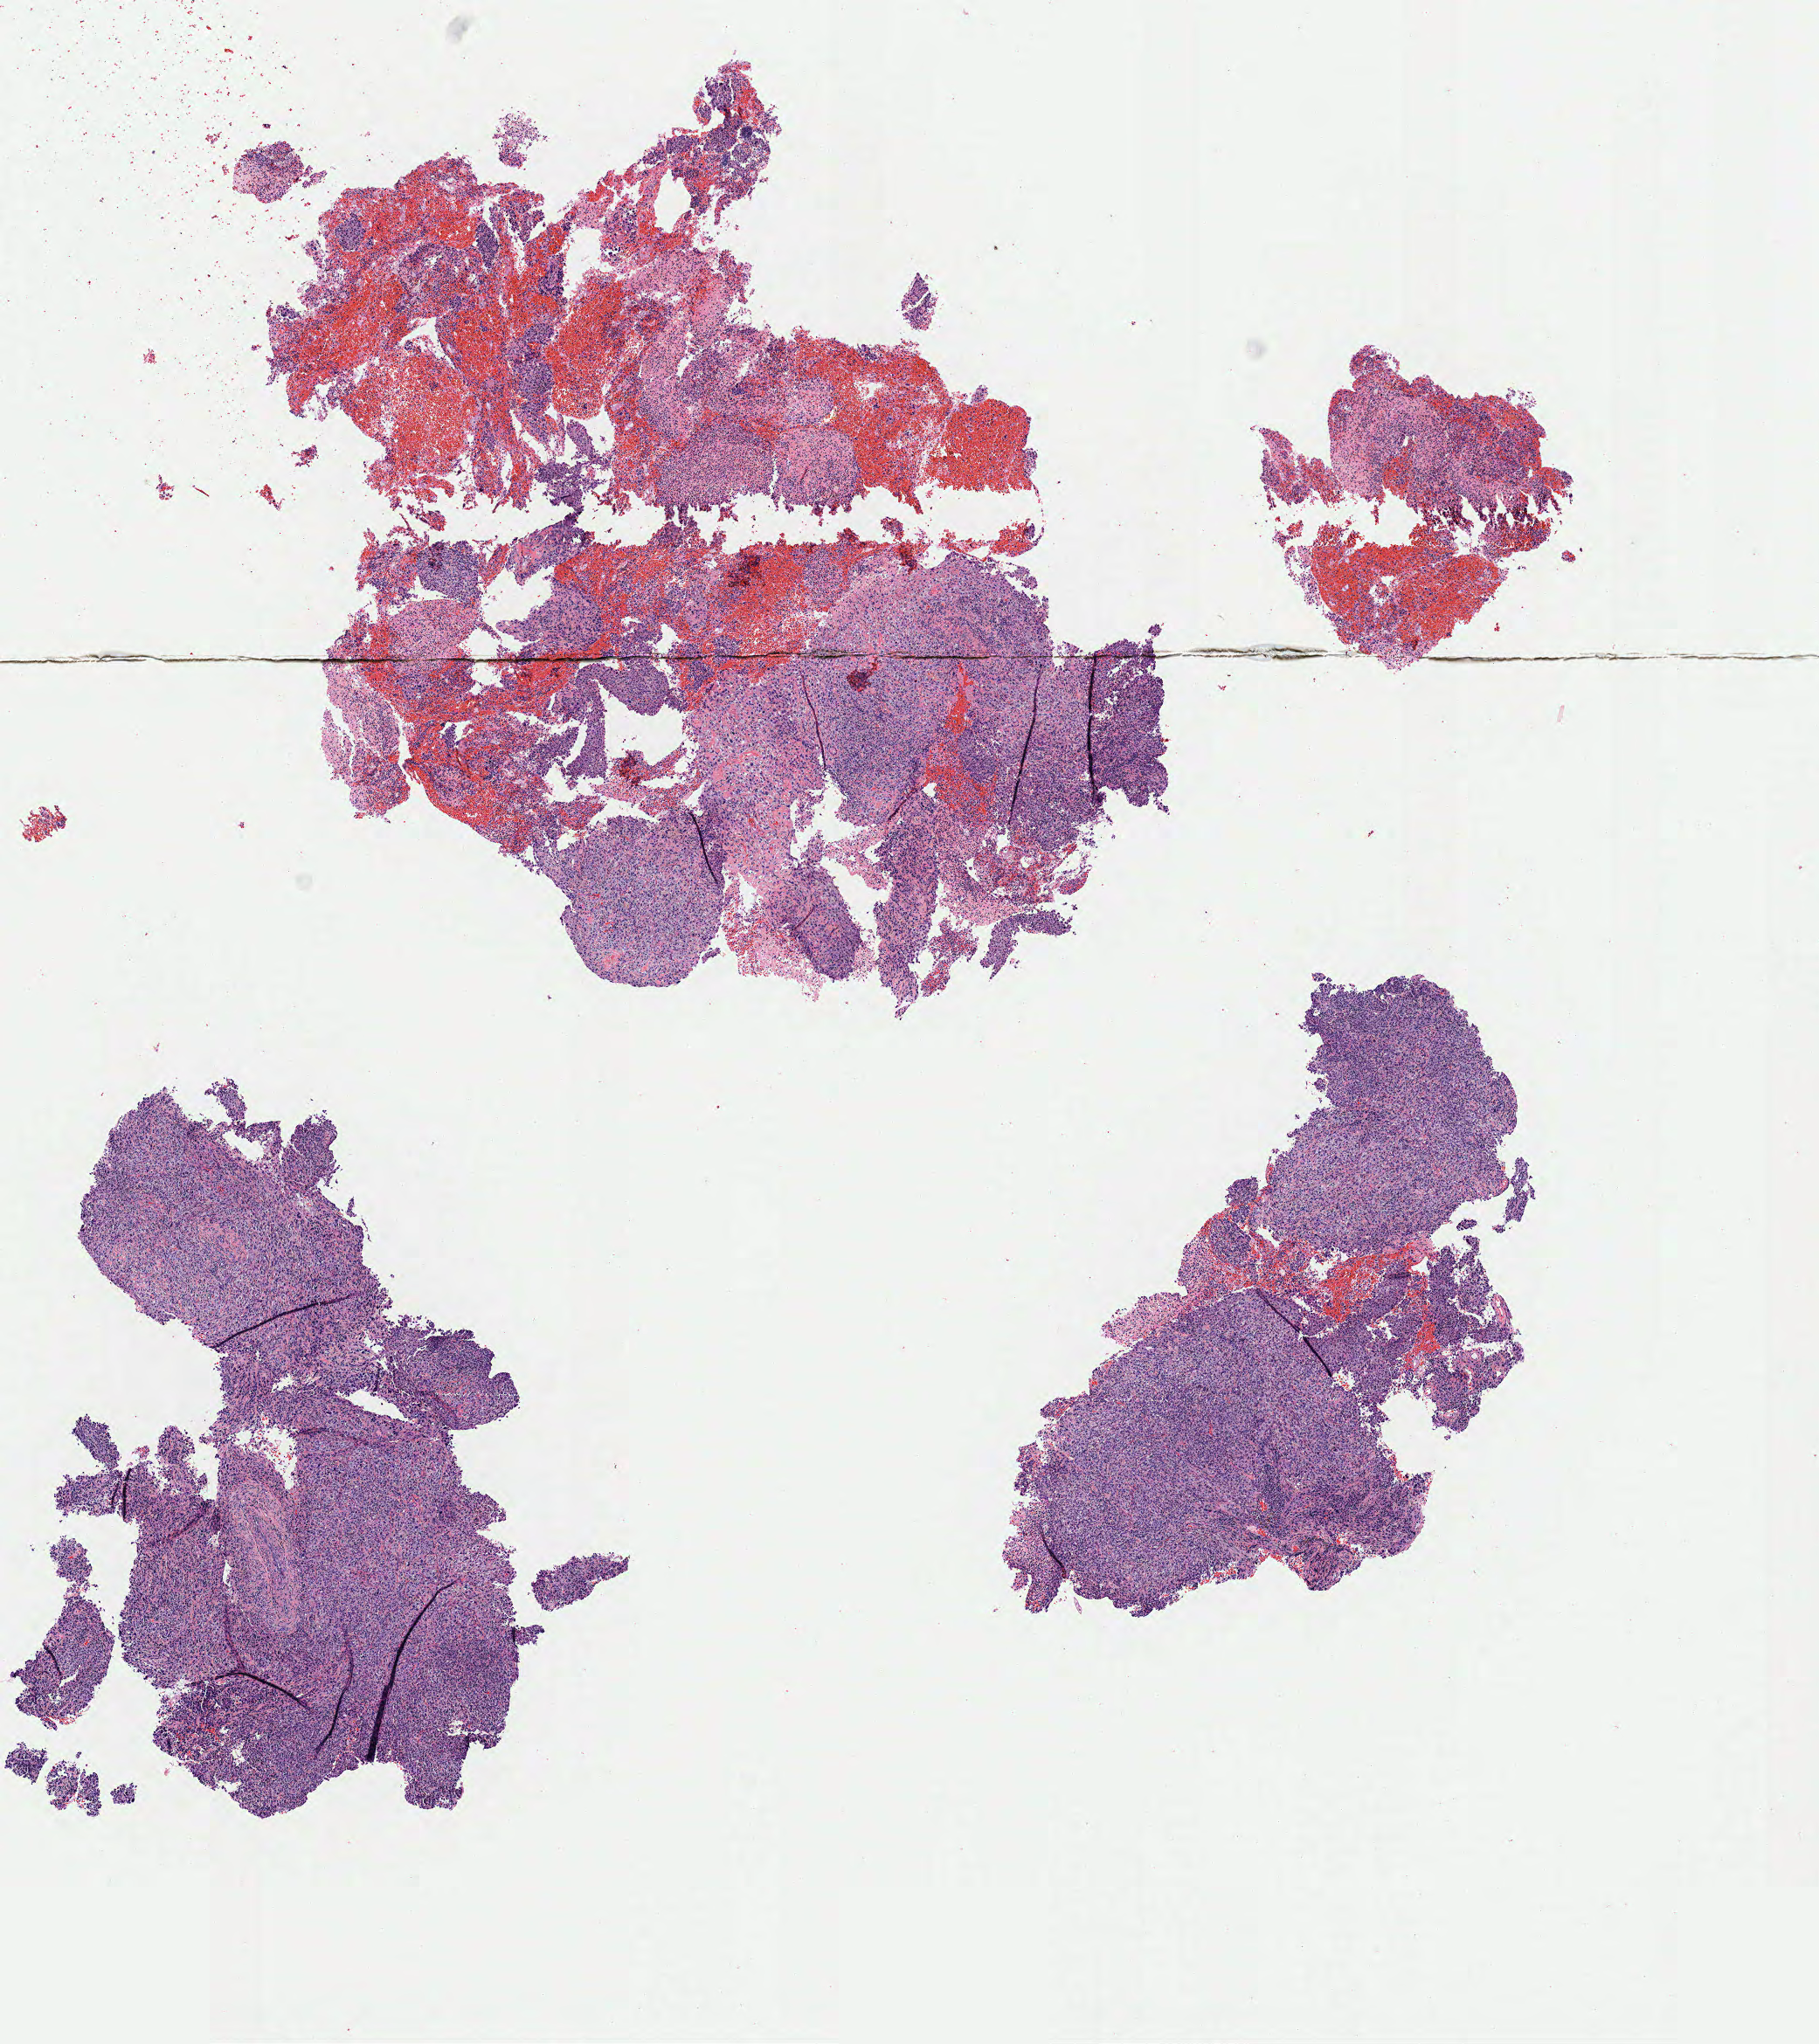
Digitized H&E-stained section, low-resolution overview of the scanned area, about 8.2 x 9.2 mm, specimen: tumor tissue, anatomic site: cervix. Patient: female, age 41 years.
• diagnosis: Squamous cell carcinoma, large cell, nonkeratinizing, NOS